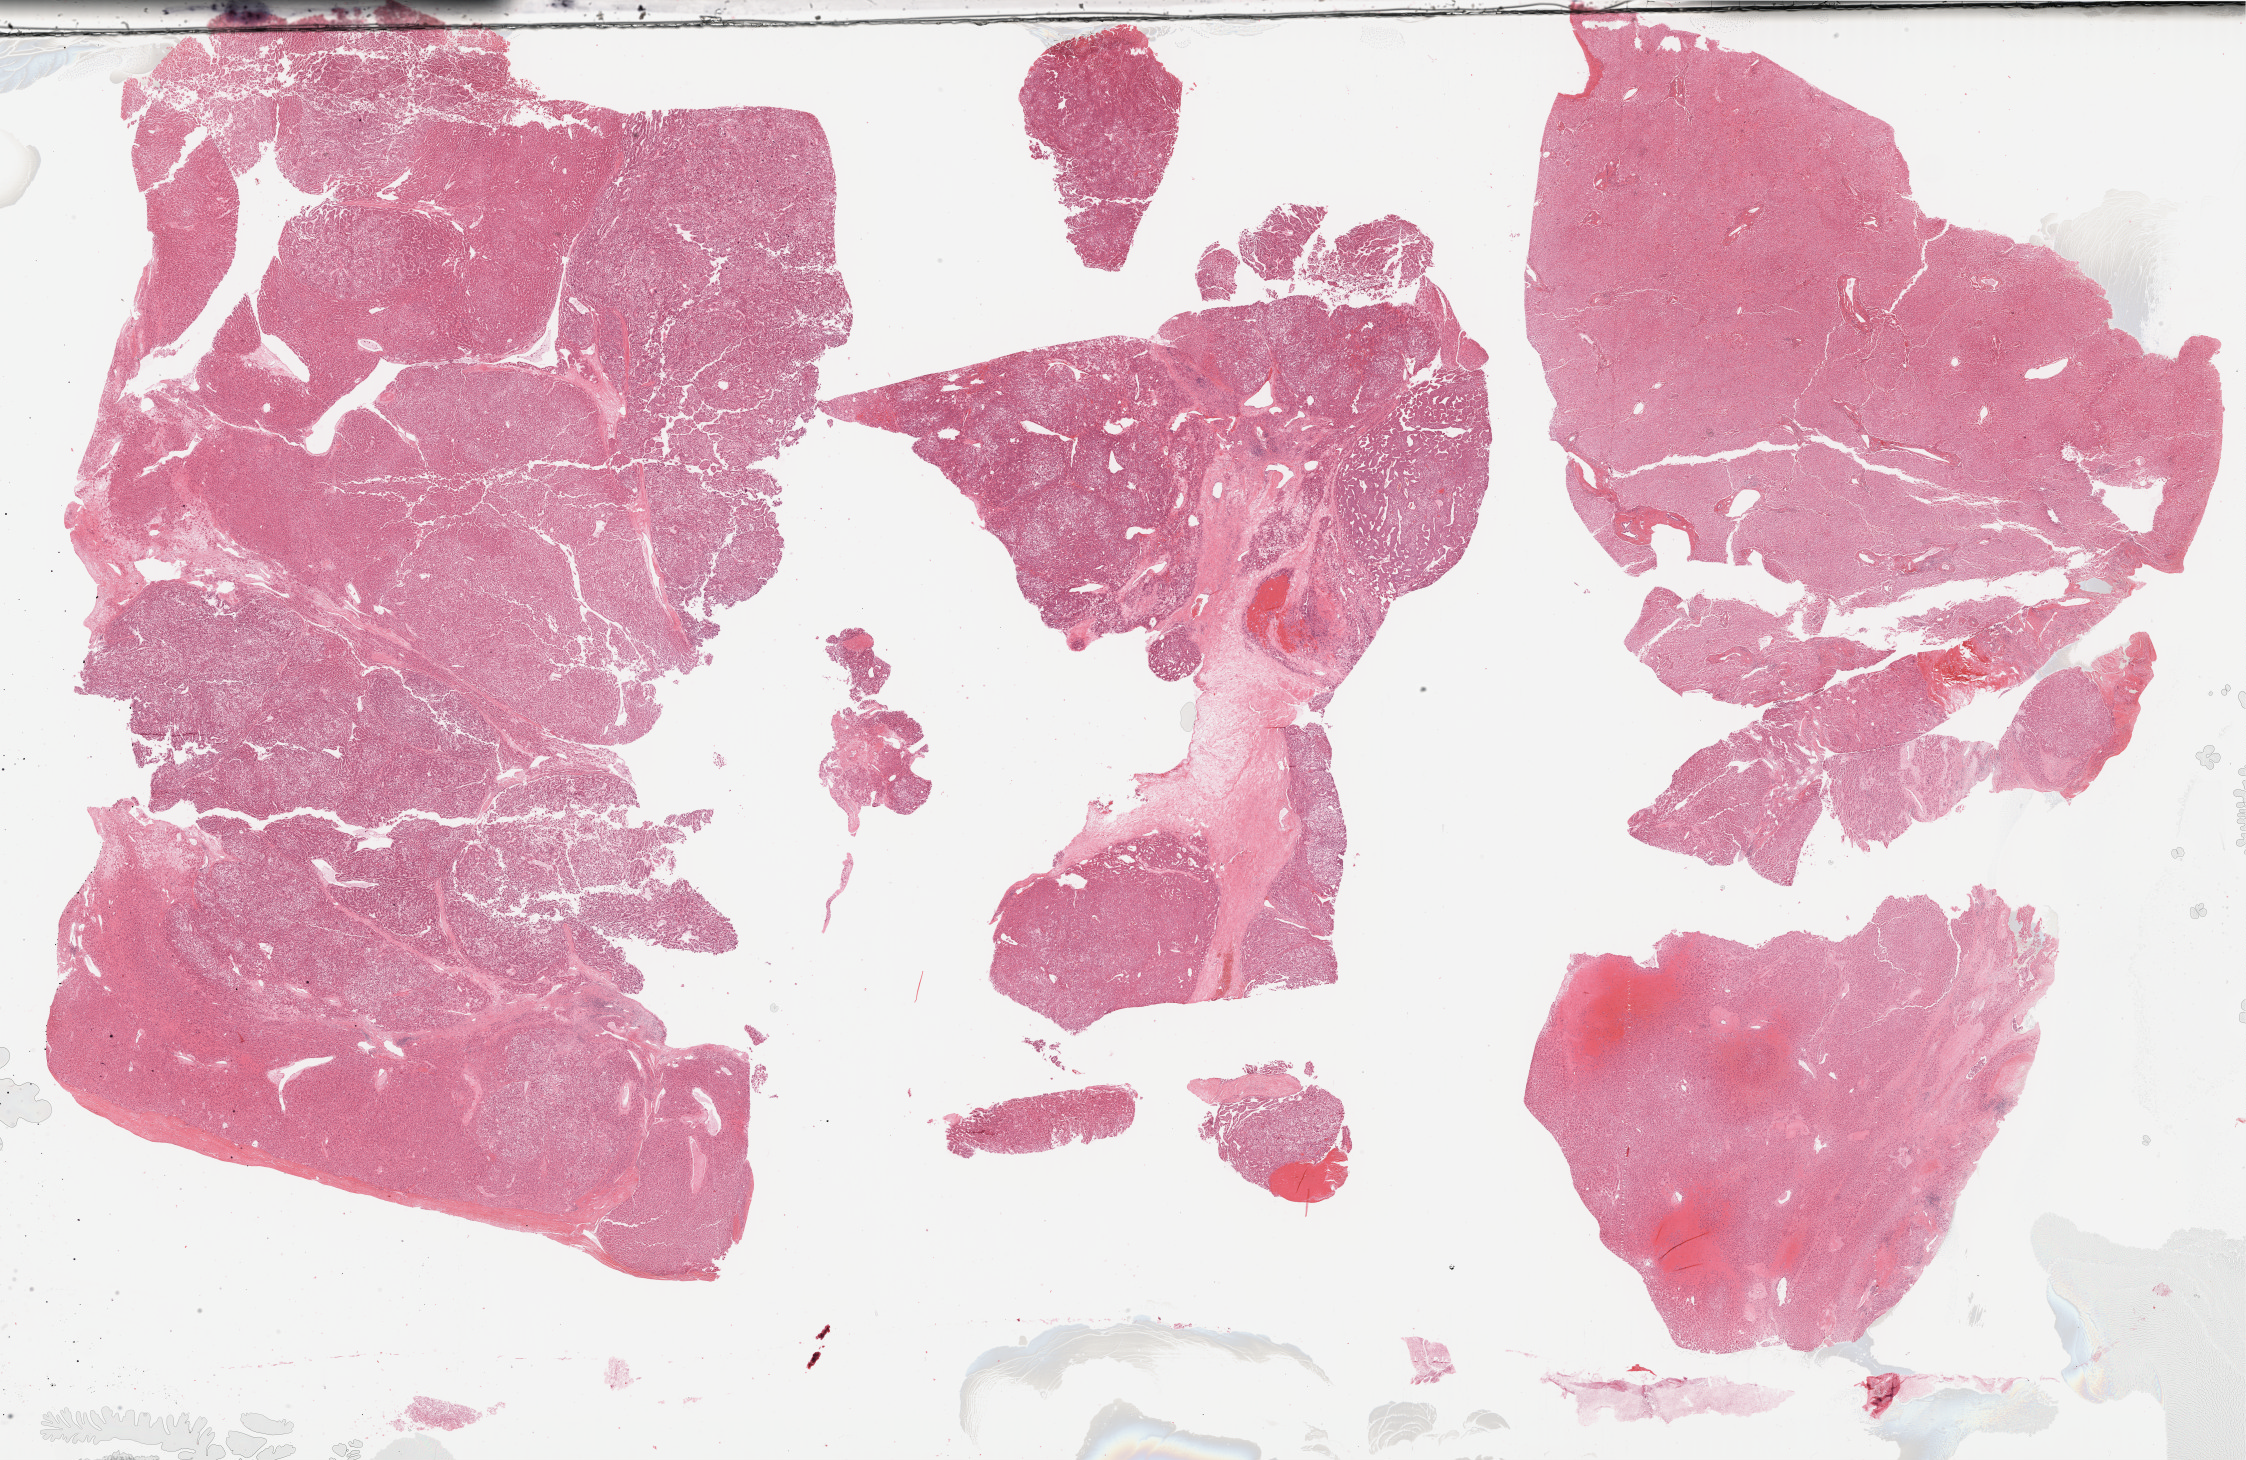
Digitized Hematoxylin and eosin (H&E) stained tissue section (whole slide) — low-resolution overview of the scanned area, about 36.4 x 23.6 mm (acquisition: 40x scan). FFPE section. Sample: primary tumour, liver. Female patient; age at initial diagnosis 72 years. Histologic grade: G2 (moderately differentiated).
• AJCC pathologic stage: I
• pathologic diagnosis: Hepatocellular carcinoma, NOS